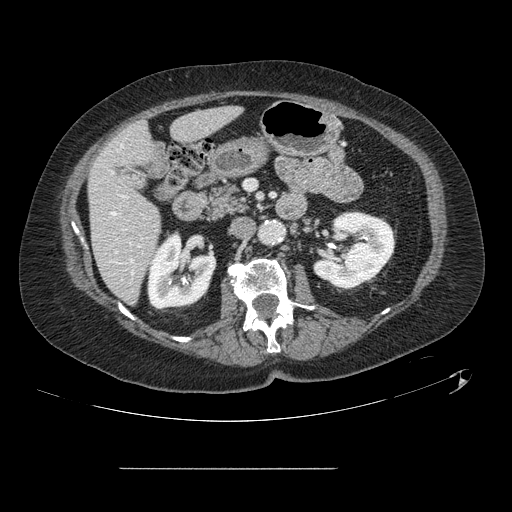
Contrast-enhanced abdominal CT, one axial slice; position 47 of 148 along the scan axis; intravenous contrast given; soft-tissue window (W 400 / L 40 HU); 2.5 mm slice thickness; 512 × 512 image matrix, field of view 439 × 439 mm. Female patient, age 75 years. Case-level facts recorded for this patient, not image findings: diagnosis: colorectal cancer liver metastases, imaged before liver resection; multiple liver metastases: no; largest metastasis: 2.4 cm; disease in both lobes: no.
Outlined on this slice (expert manual segmentation):
- hepatic veins: bounding box (x1, y1, x2, y2) in pixels: (112, 212, 133, 263)
- liver: (89, 107, 239, 303)
- planned liver remnant (the part of the liver to remain after resection): (89, 107, 239, 303)